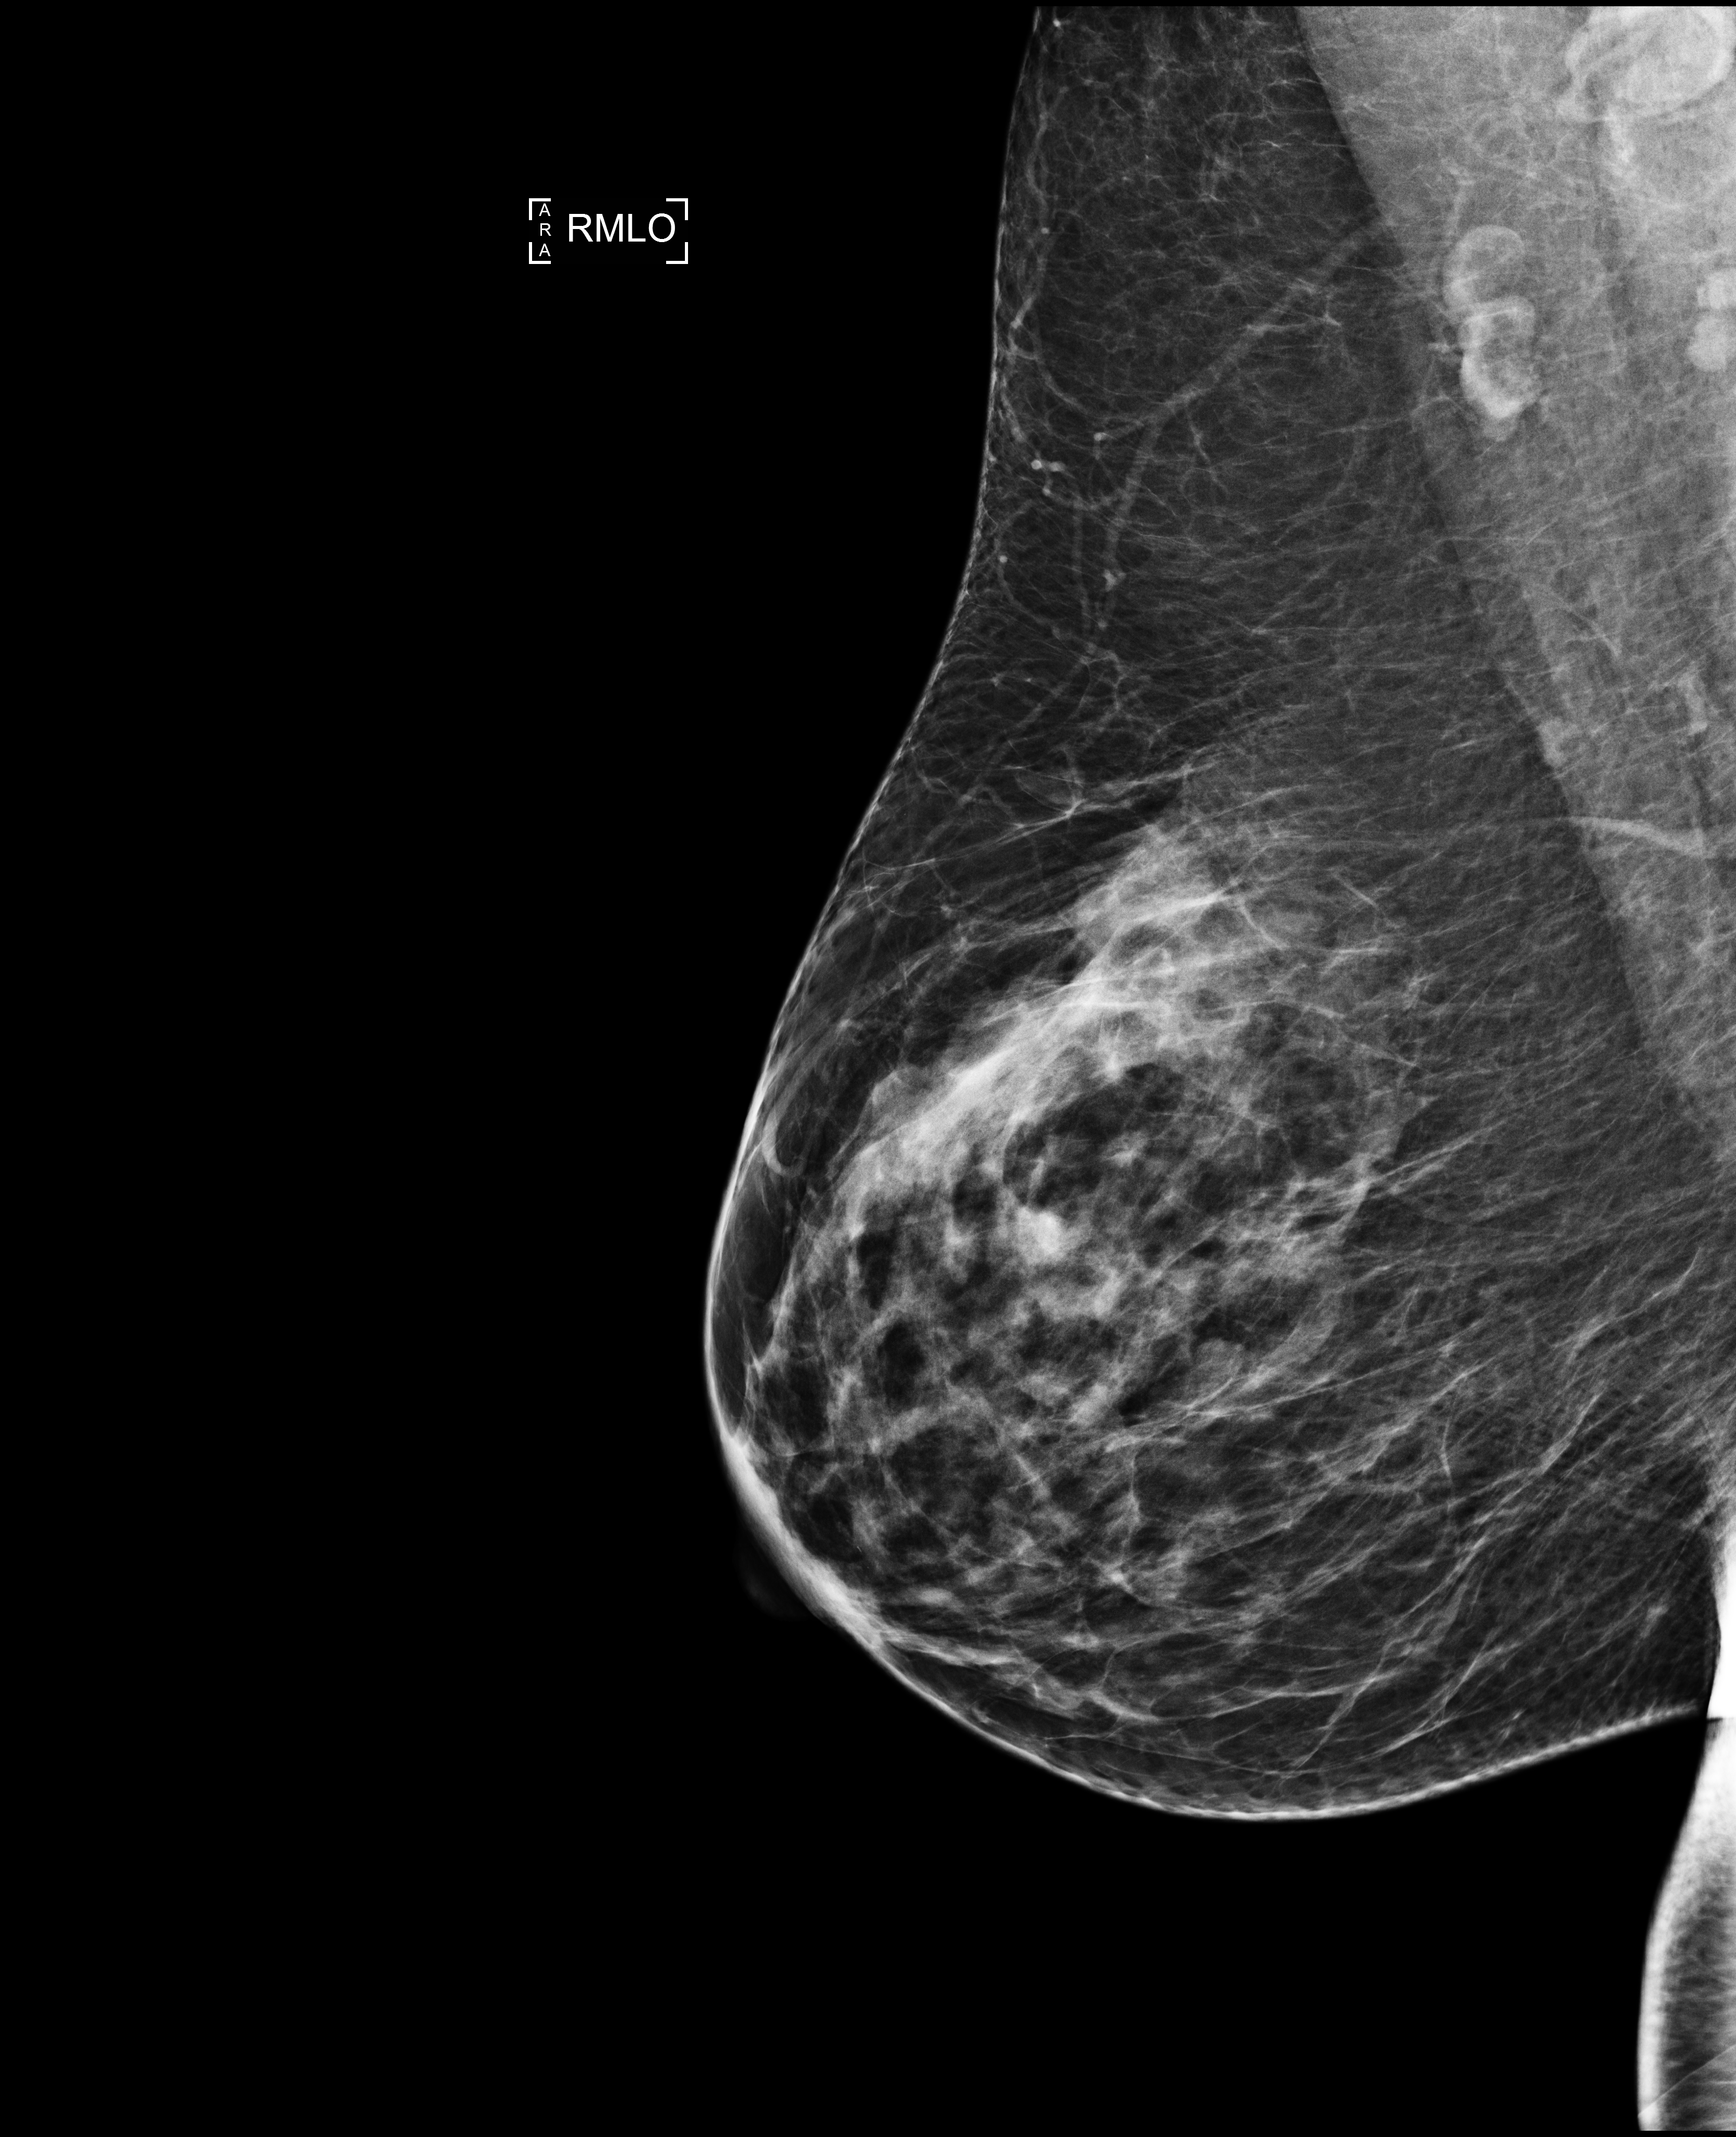
Digital mammogram (FFDM), right breast, MLO view, annual screening mammography examination. Patient aged 51 years (female).
Breast density at the screening exam (both breasts): heterogeneously dense (BI-RADS density category c). Final BI-RADS assessment for this screening round (tomosynthesis exam, both breasts): category 1. Recall: no recall after this screen.